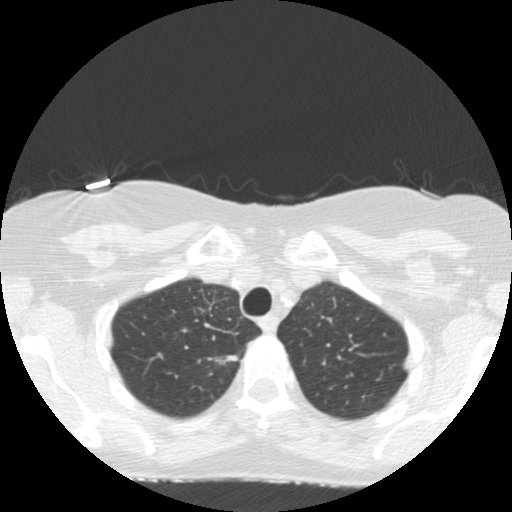
Low-dose screening chest CT, one axial slice; slice 127 of 155 in the series (ordered by position); reconstruction kernel STANDARD; 120 kVp; lung window (W 1500 / L -600 HU); 2.5 mm slice thickness; 512 × 512 image matrix, field of view 300 × 300 mm.
Annotated regions visible in this slice (manually delineated by an expert):
- lesion 1 (tumor, upper lobe of right lung): bounding box (x1, y1, x2, y2) in pixels: (215, 355, 238, 365)